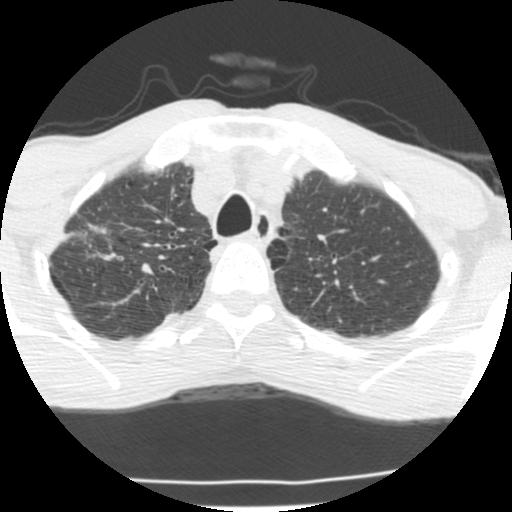
Low-dose screening chest CT, one axial slice; slice 176 of 214 in the series (ordered by position); reconstruction kernel STANDARD; lung window (W 1500 / L -600 HU); 2.5 mm slice thickness; 512 × 512 image matrix, field of view 283 × 283 mm.
Annotated regions visible in this slice (outlined manually by an expert reader):
- lesion 1 (tumor, upper lobe of right lung): bounding box (x1, y1, x2, y2) in pixels: (88, 224, 107, 234)